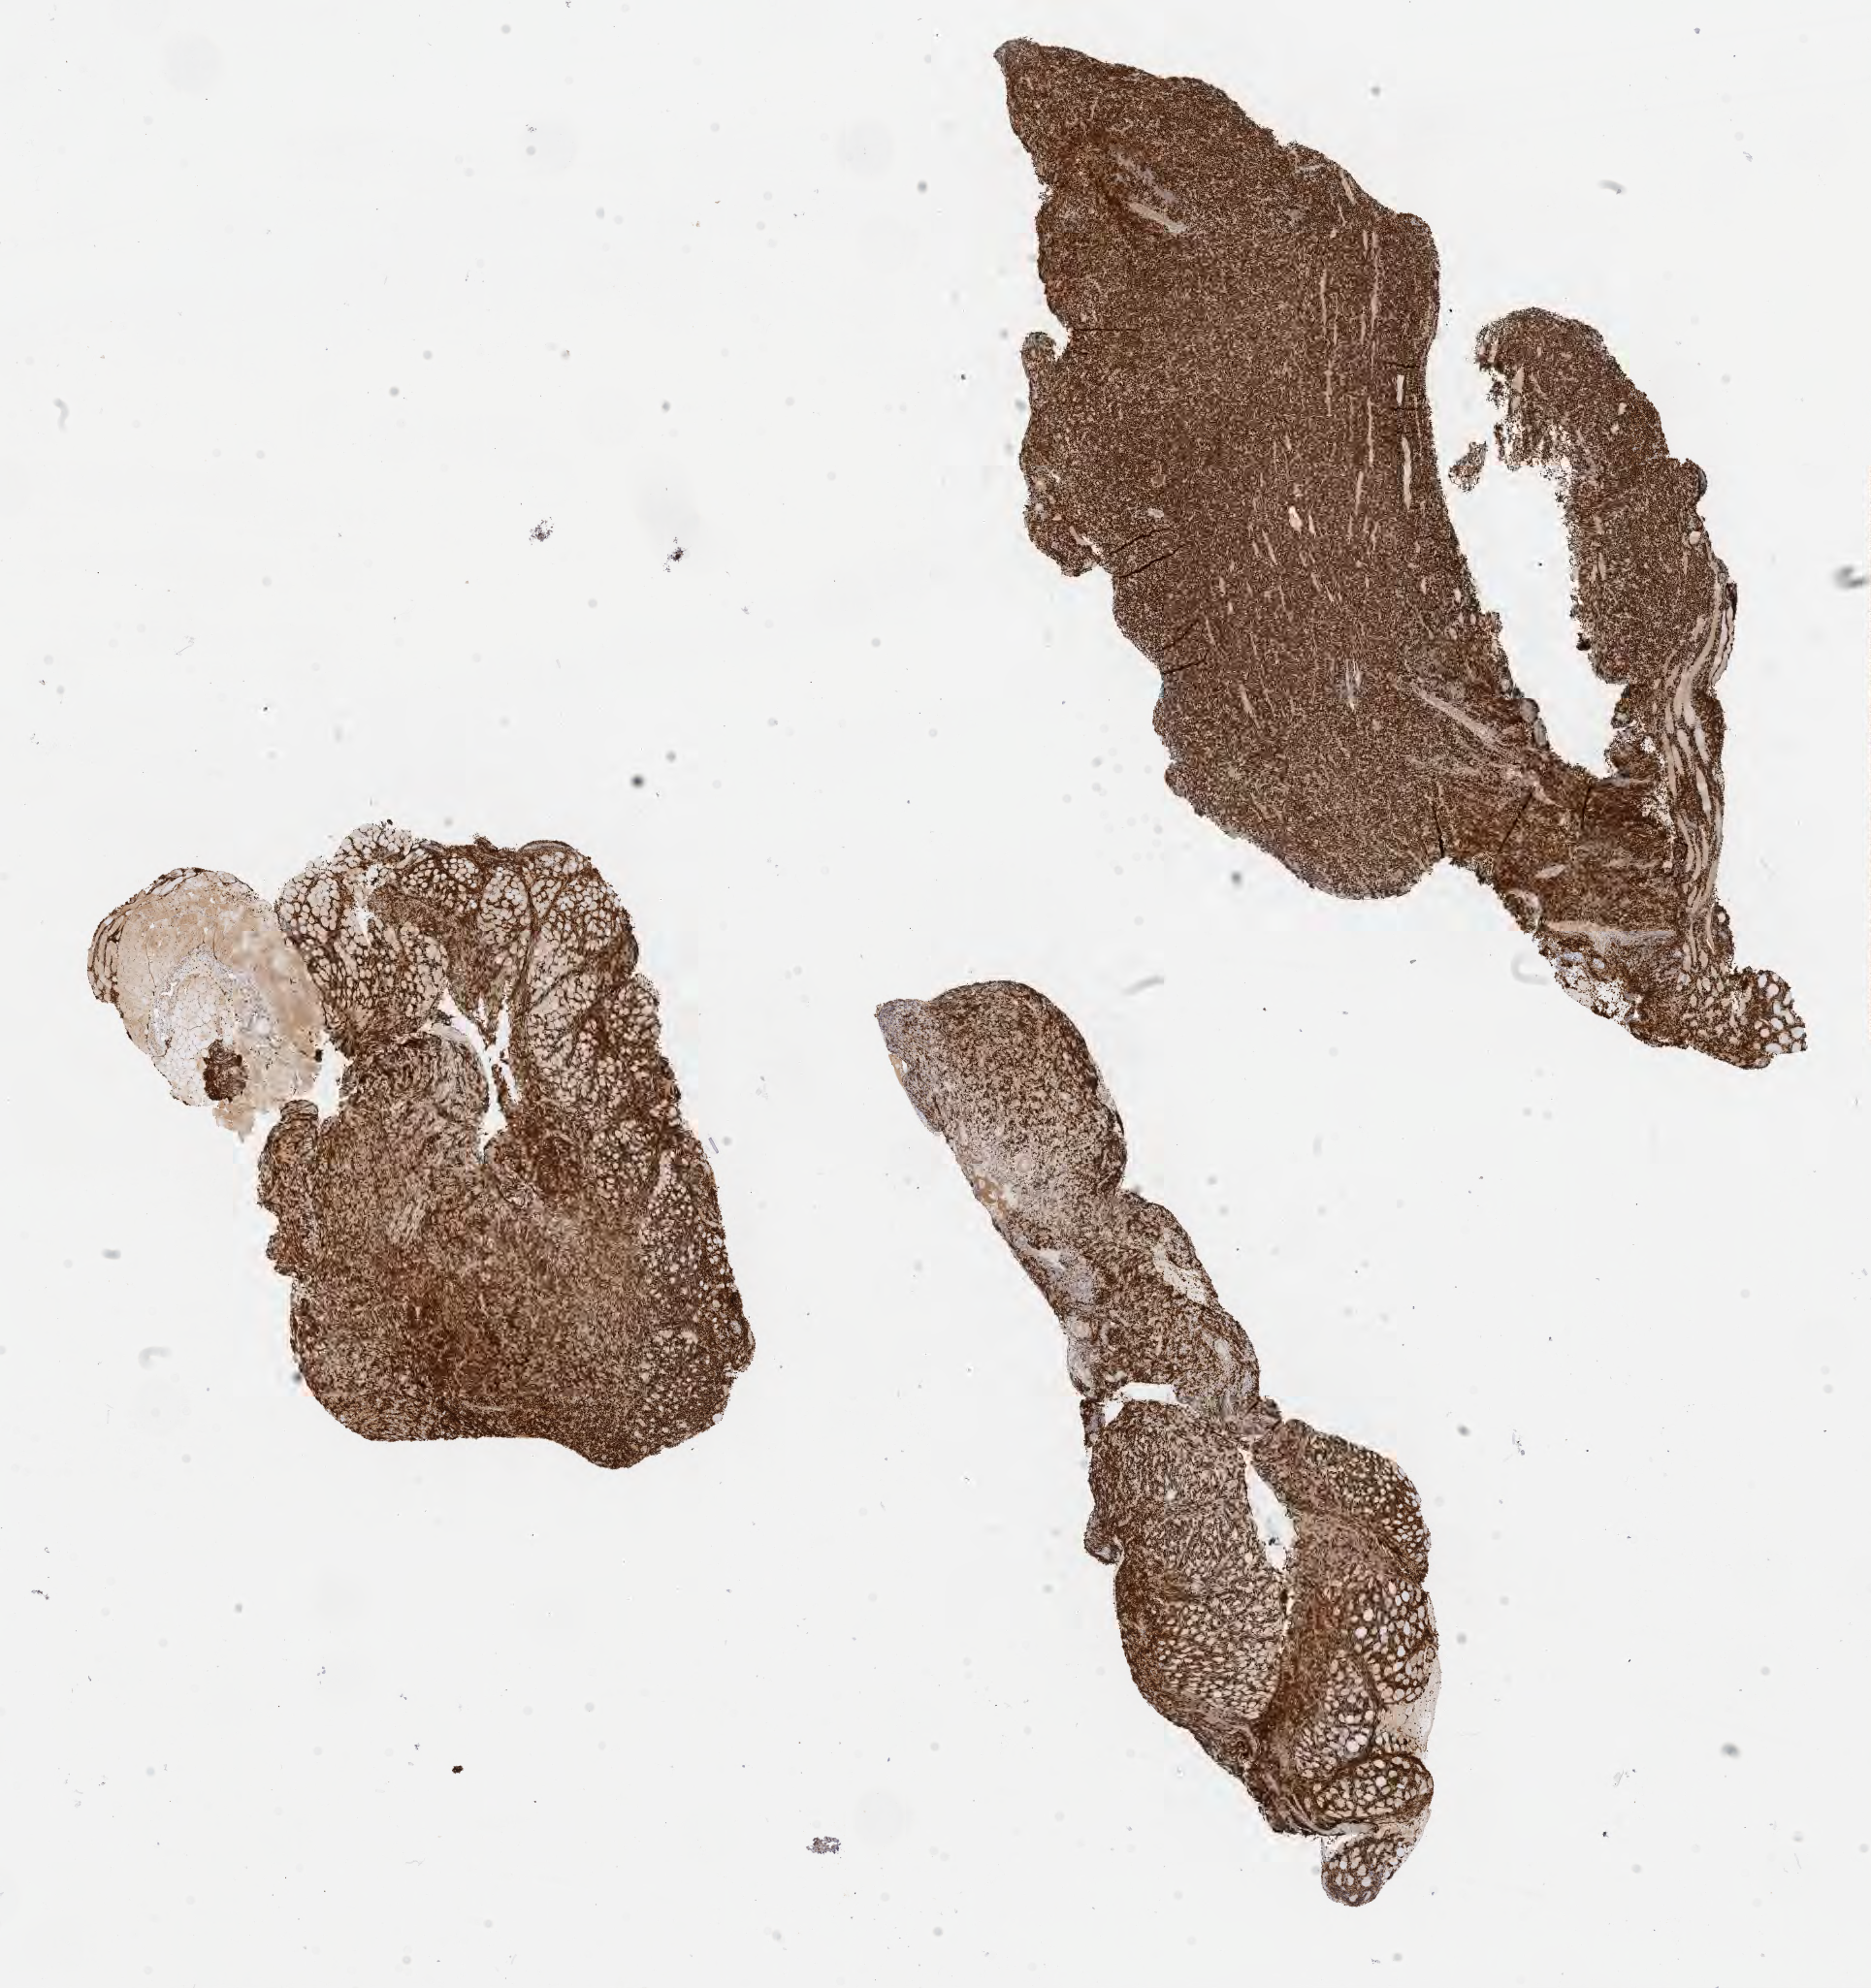
Whole-slide image, immunohistochemical stain for BCL6, a low-resolution overview of the entire scanned area, about 15.6 x 16.6 mm; specimen: tumor tissue; site: lymph node of head and neck. Patient: male, age 55 years.
Diagnosis: Burkitt lymphoma, NOS.